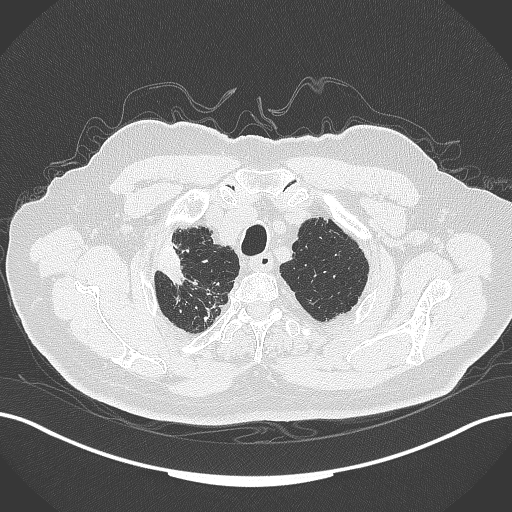
Chest CT, one axial slice. Position 315 of 389 along the scan axis. Reconstruction kernel B70f. 120 kVp. Lung window (W 1500 / L -600 HU). 1 mm slice thickness. 512 × 512 image matrix, field of view 400 × 400 mm. Patient: male, 72 years. Case-level facts recorded for this patient, not image findings: clinical TNM (as recorded): T1a N0 M0.
Outlined on this slice (rectangle marked by the reading radiologist):
- lung tumour (recorded histology: squamous cell carcinoma): bounding box [x1, y1, x2, y2] px = [159, 232, 193, 284]